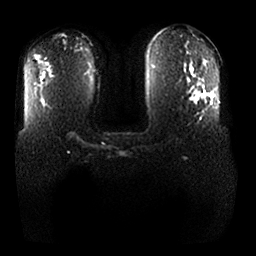
Breast MRI, one axial slice. Slice 20 of 25 in the series (ordered by position). Diffusion-weighted series; image 2 of 4 stored at this slice position (different b-values; order by instance number). 1.5 T. 4 mm slice thickness. 256 × 256 image matrix, field of view 370 × 370 mm. Female patient.
Annotated regions visible in this slice (outlined manually by an expert reader):
- tumour on diffusion-weighted imaging: box from (x=193, y=95) to (x=198, y=101) px